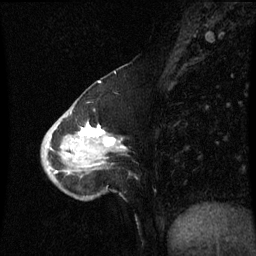
Breast MRI (dynamic contrast-enhanced), one sagittal slice; dynamic contrast-enhanced series, image 2 of 3 at this slice position (ordered by acquisition); 1.5 T; TE 4.2 ms, TR 8.9 ms; 2 mm slice thickness; 256 × 256 image matrix, field of view 200 × 200 mm. Patient: female, 50 years. Case-level facts recorded for this patient, not image findings: setting: breast cancer imaged before/during neoadjuvant chemotherapy; receptor status: HR-positive, HER2-negative.
Annotated regions visible in this slice (semi-automatic segmentation, software-assisted and operator-edited):
- analysis volume of interest (the breast-tissue region the enhancement analysis was run in; not a lesion): bounding box [x1, y1, x2, y2] px = [43, 100, 126, 201]
- tumour enhancement mask (voxels above the 70 % enhancement threshold inside the analysis volume of interest): [79, 126, 124, 147]